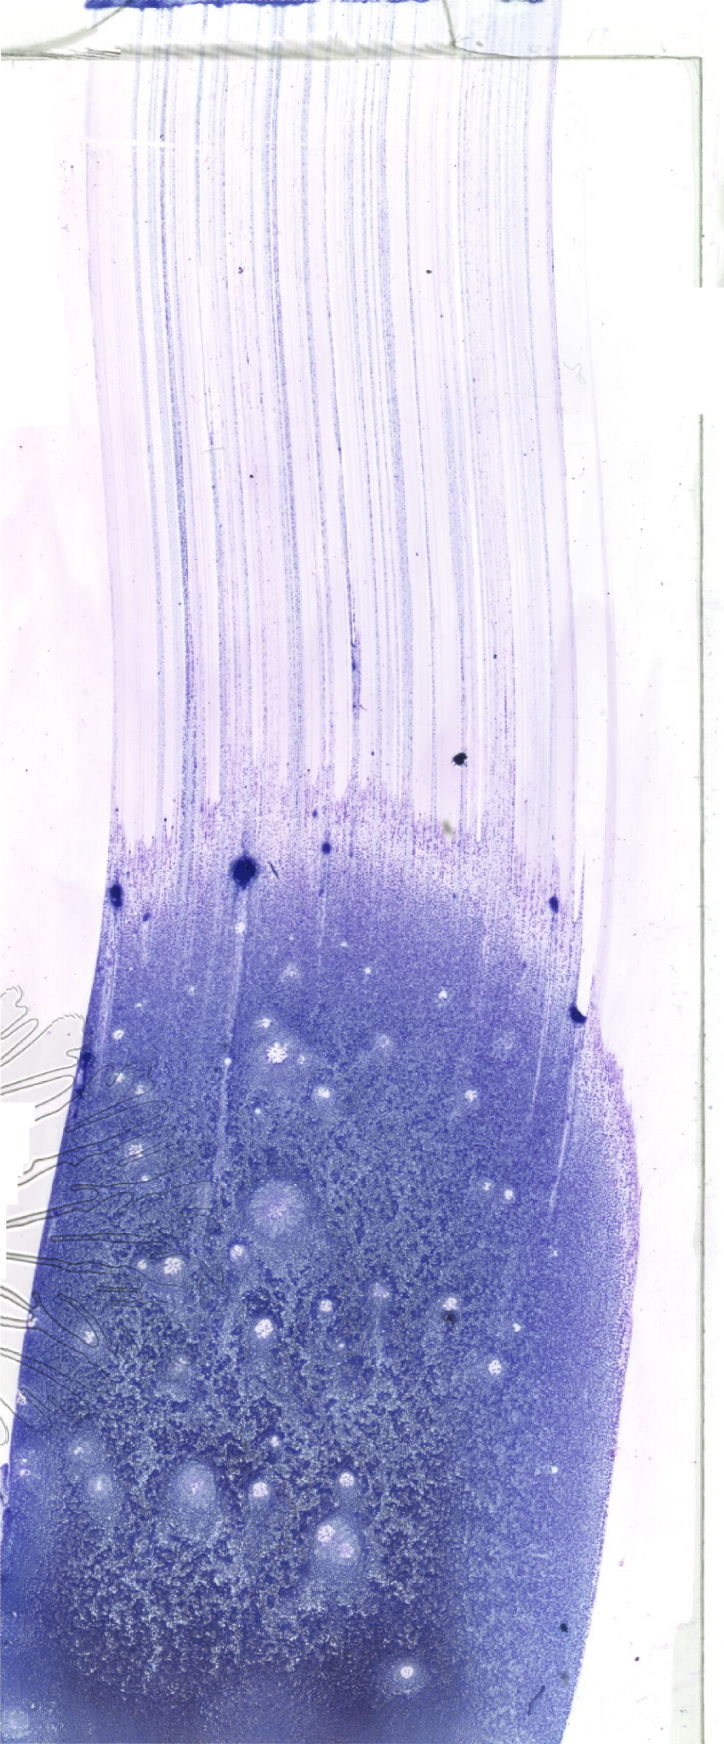
May-Grünwald-Giemsa (MGG)-stained marrow aspirate smear (whole slide), low-resolution overview of the scanned area, about 20.5 x 49.4 mm. Patient sex: male.
Diagnosis: Acute Myelomonocytic Leukemia with Abnormal Eosinophils.